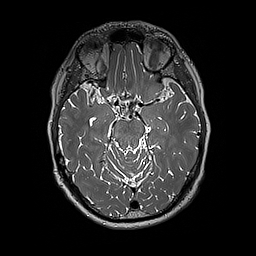
Brain MRI from a brain-tumour surgery series, one axial slice; slice 119 of 192 in the series (ordered by position); 1 mm slice thickness; 256 × 256 image matrix, field of view 250 × 250 mm. From the clinical record (not read from this slice): histopathology: Glioblastoma; WHO grade: 4; IDH mutation: no.
Annotated regions visible in this slice (outlined manually by an expert reader):
- tumour: bounding box (x1, y1, x2, y2) in pixels: (140, 85, 171, 101)